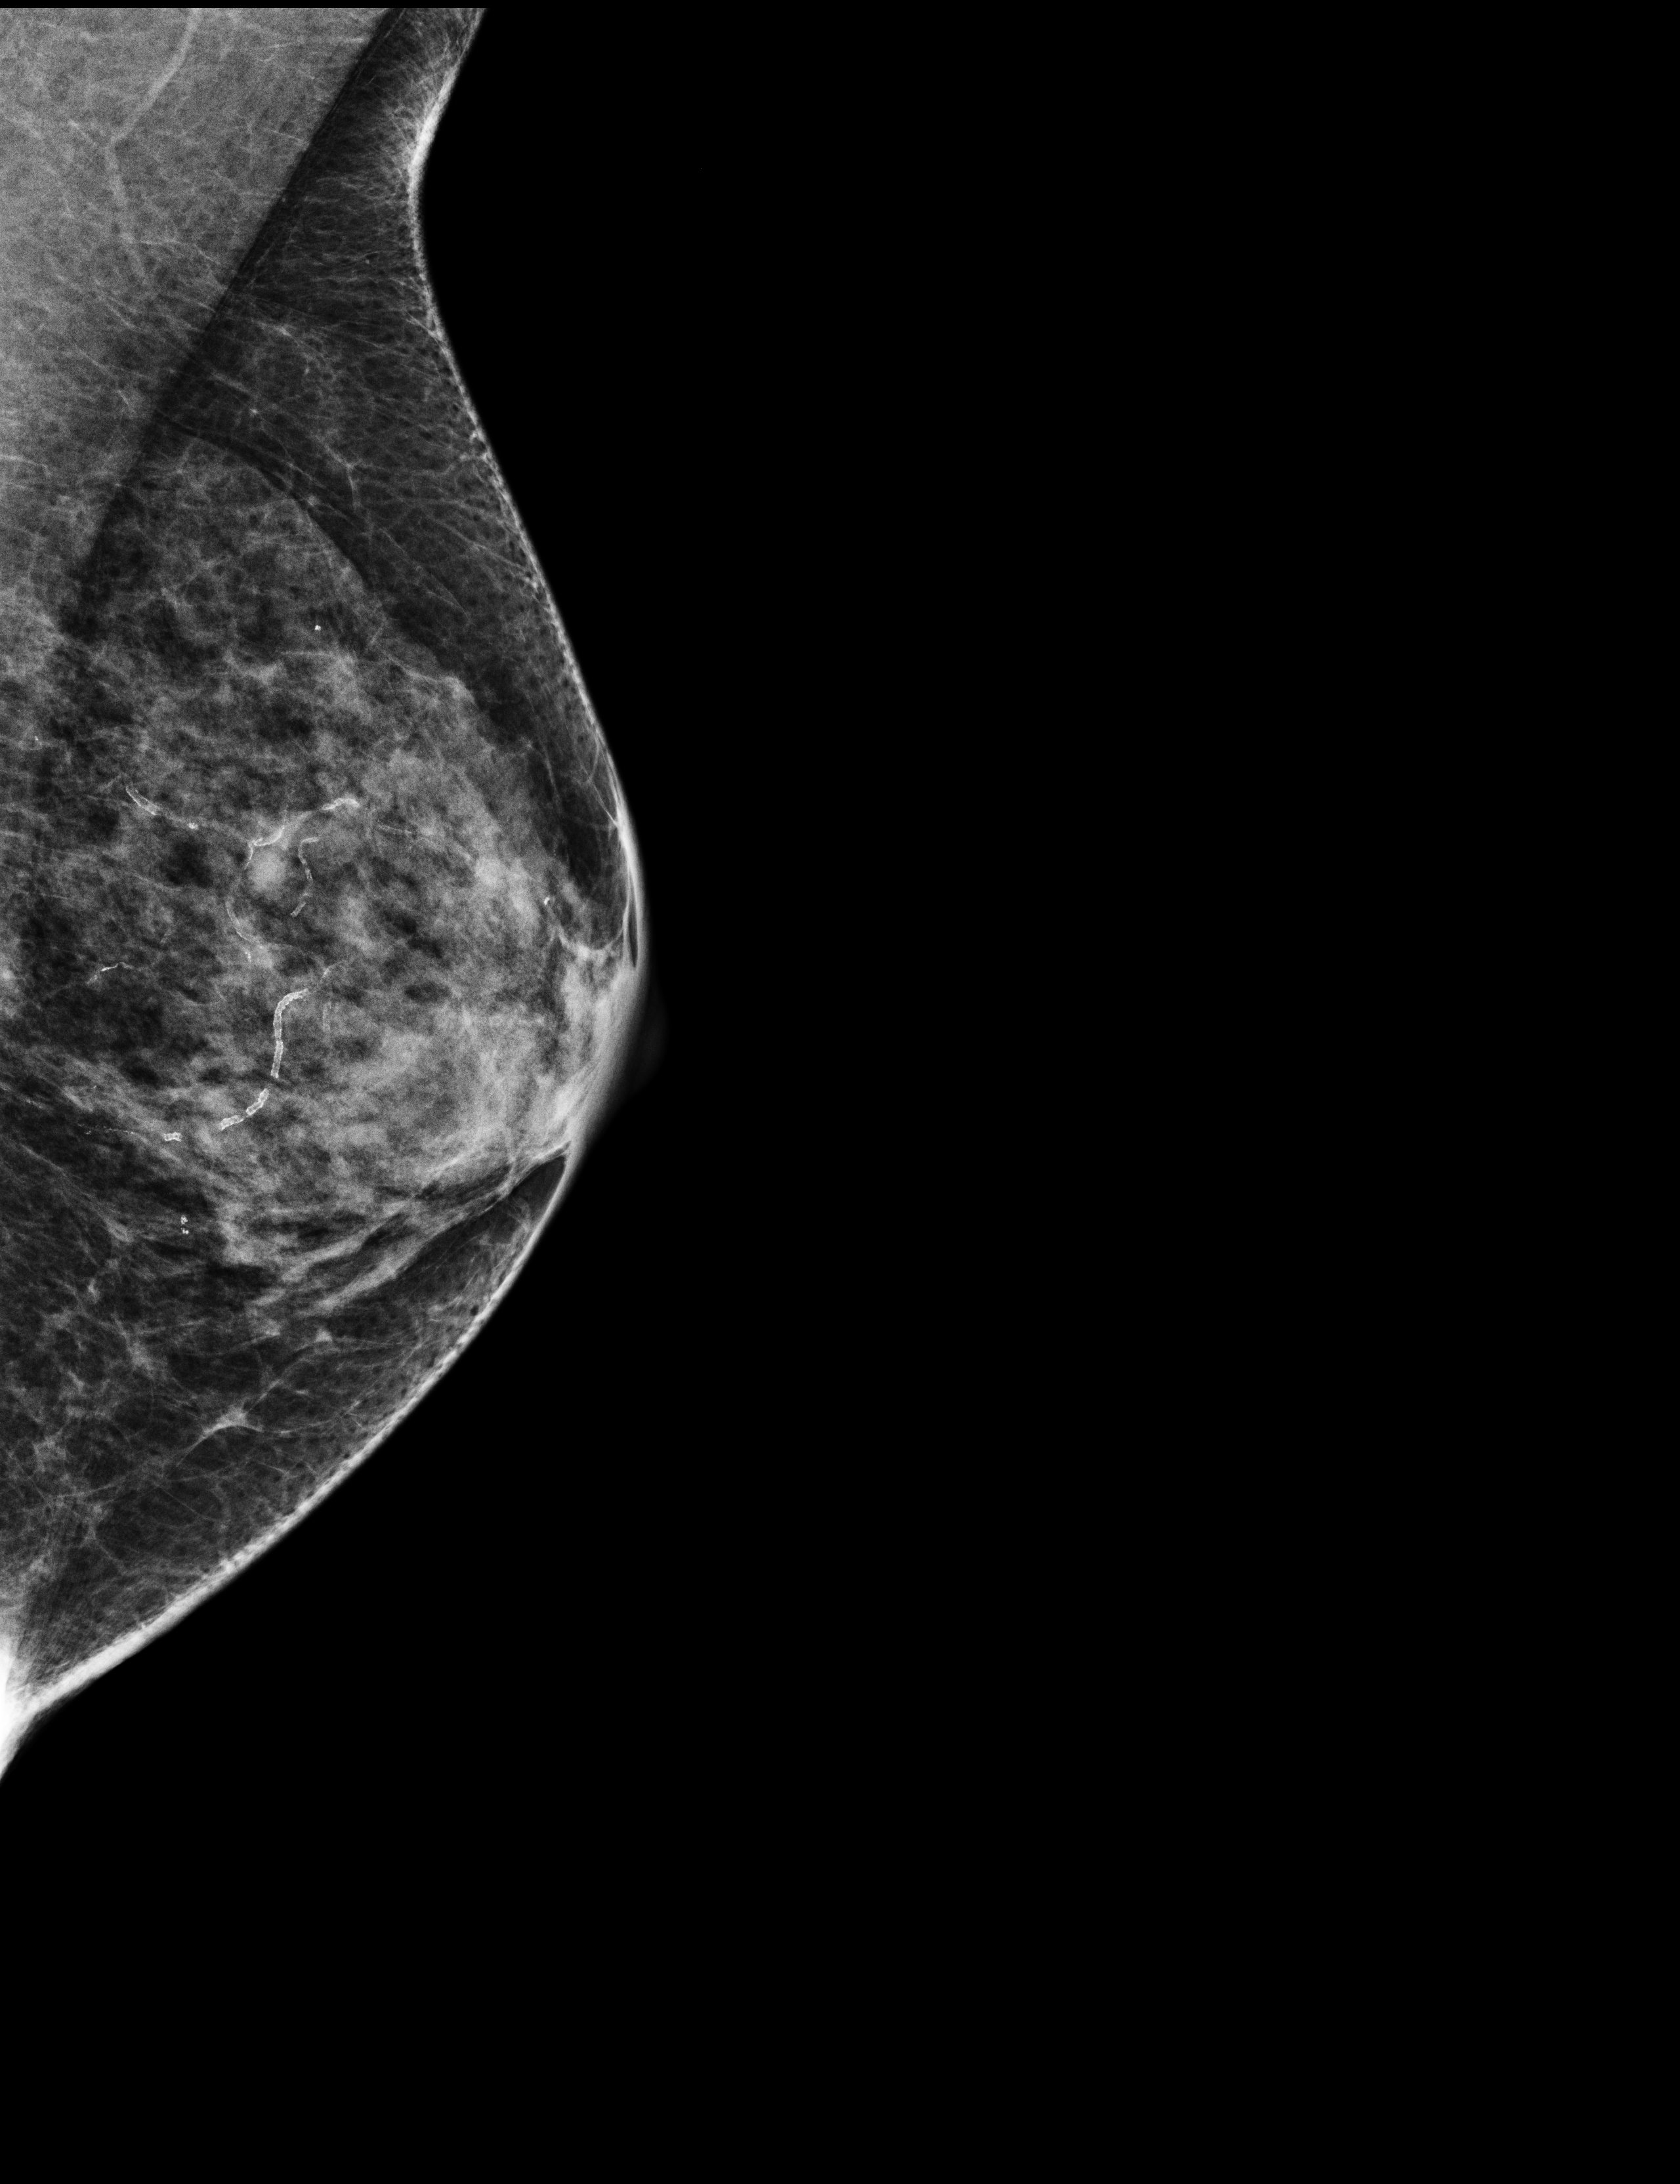
Annual screening mammography examination. Female patient, age 65 years.
Image type: full-field digital mammogram. Breast: left. Projection: MLO view.